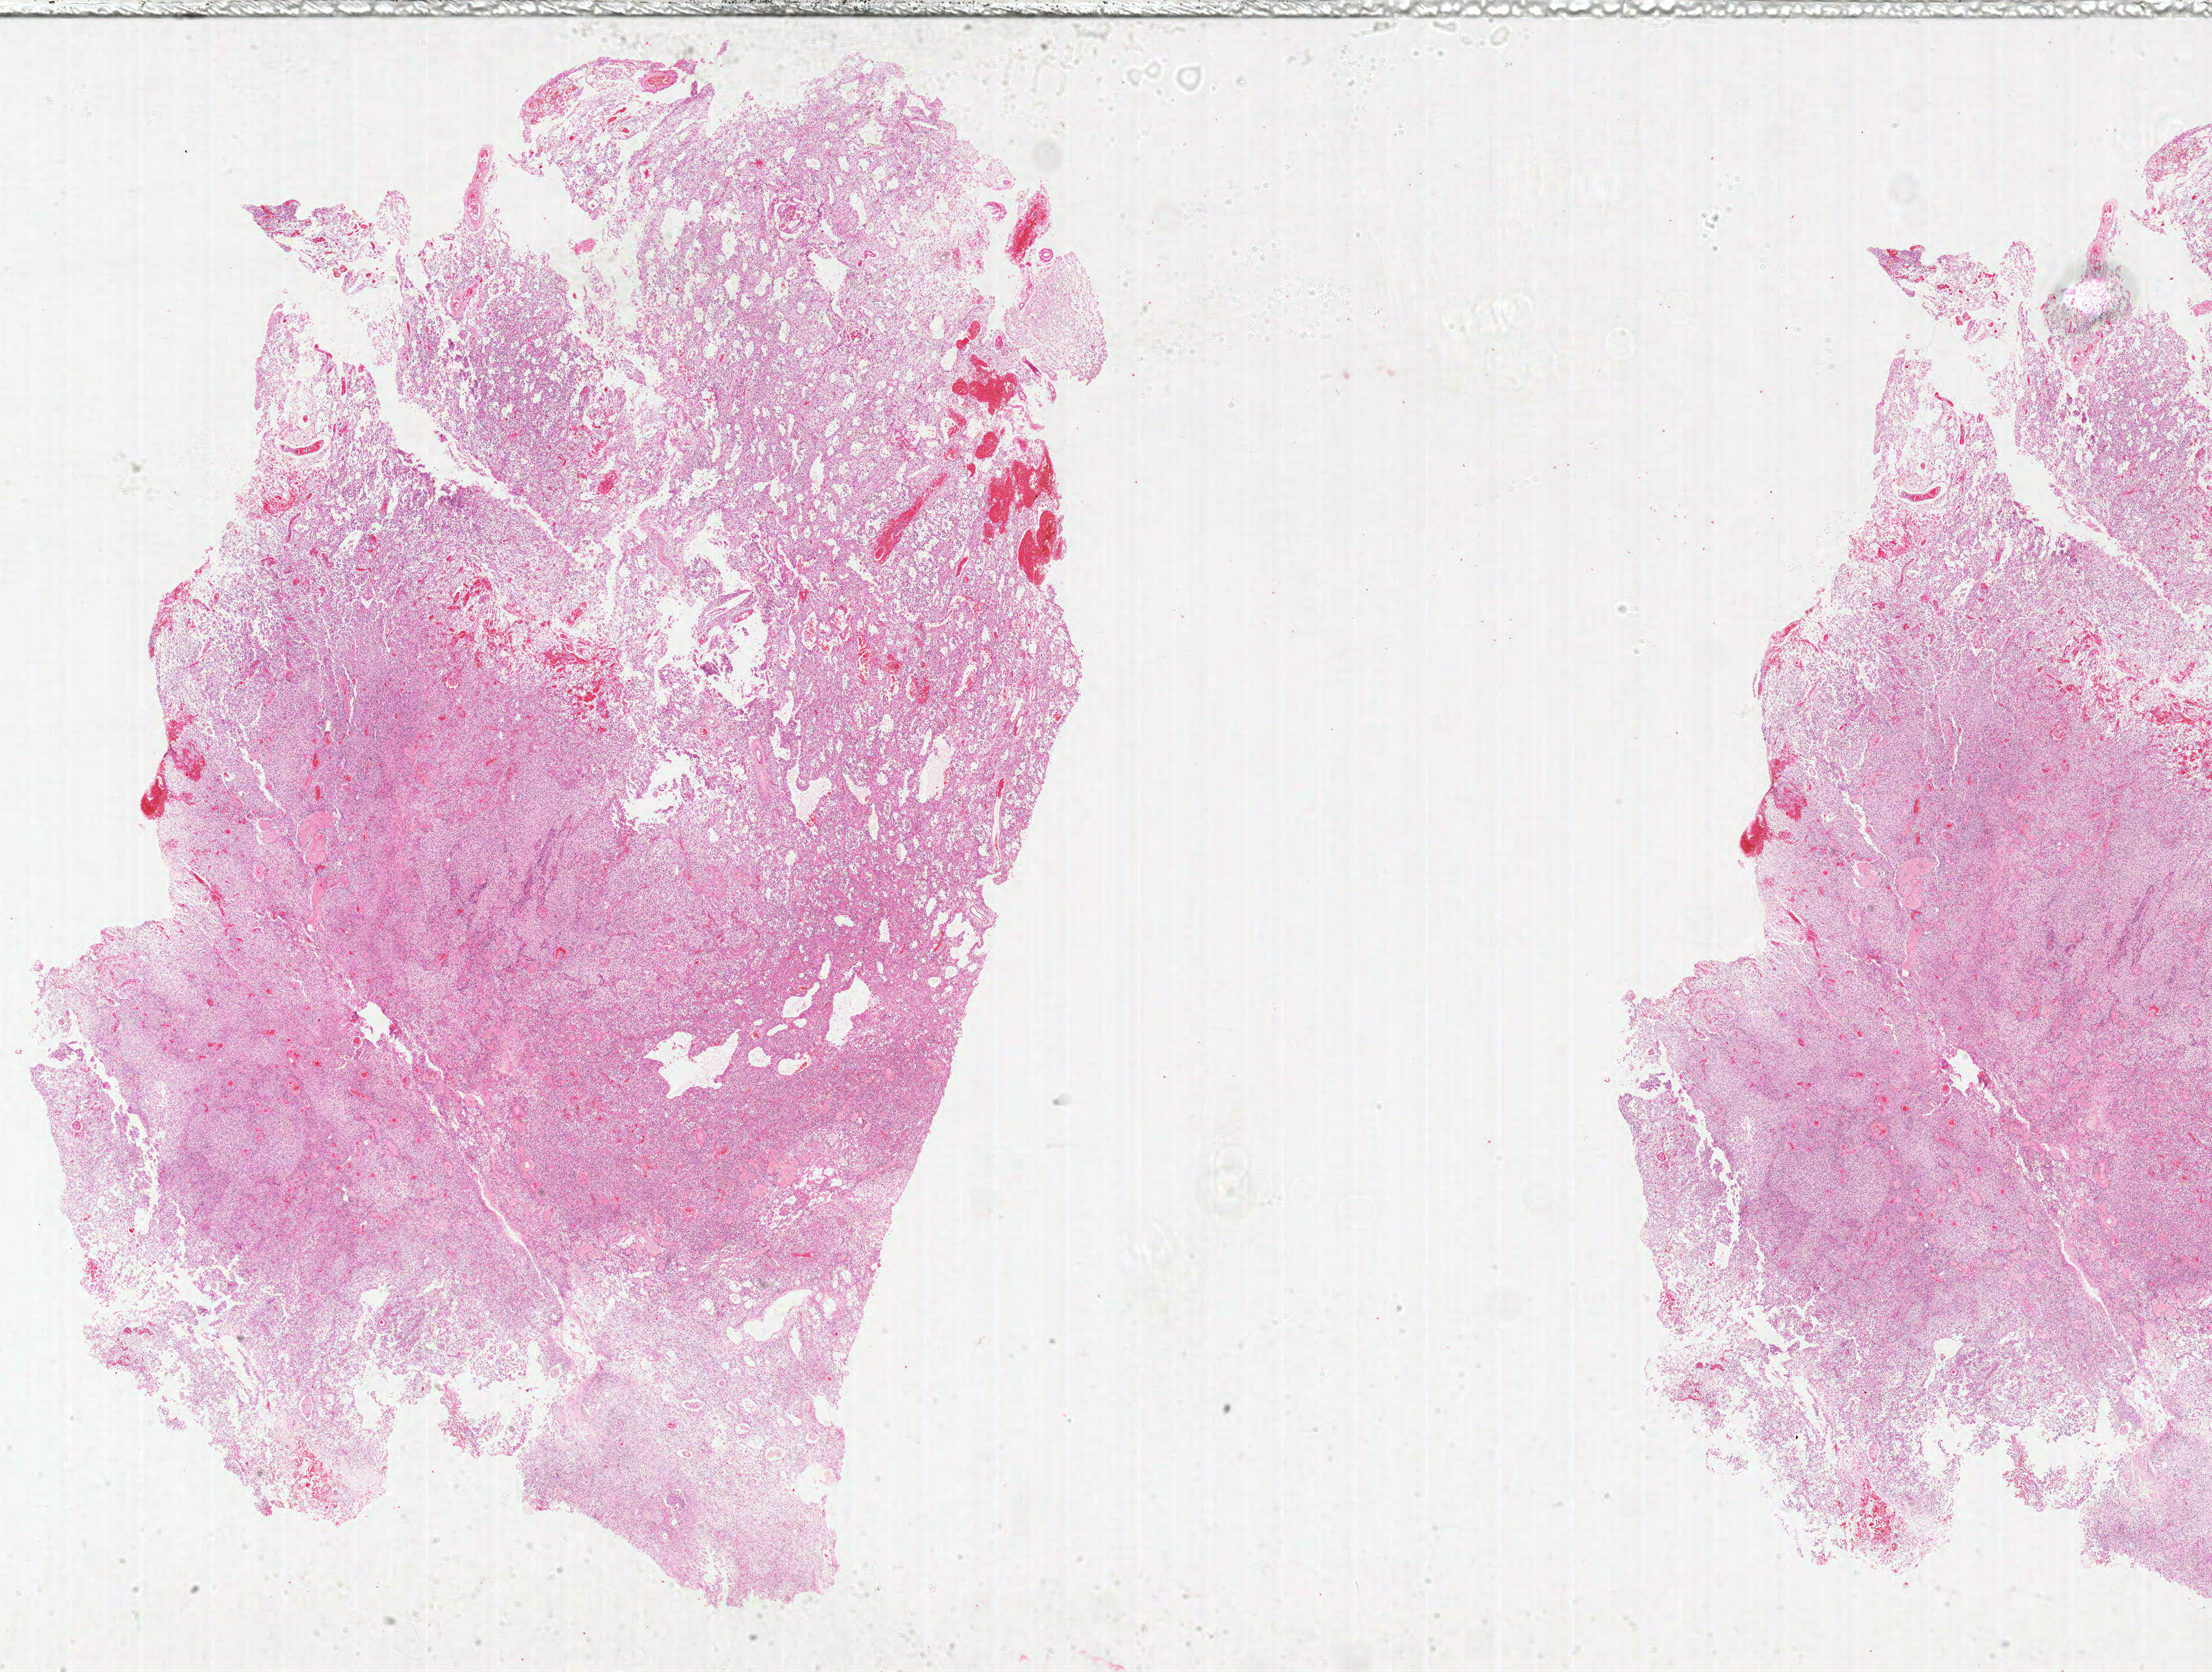
Hematoxylin and eosin (H&E) stained whole-slide image, whole scanned area (about 31.0 x 23.4 mm, from a 20x scan) shown as a low-resolution overview. FFPE section. Primary tumour sample from the brain. Female, age 45 years at initial diagnosis.
• pathologic diagnosis: Glioblastoma